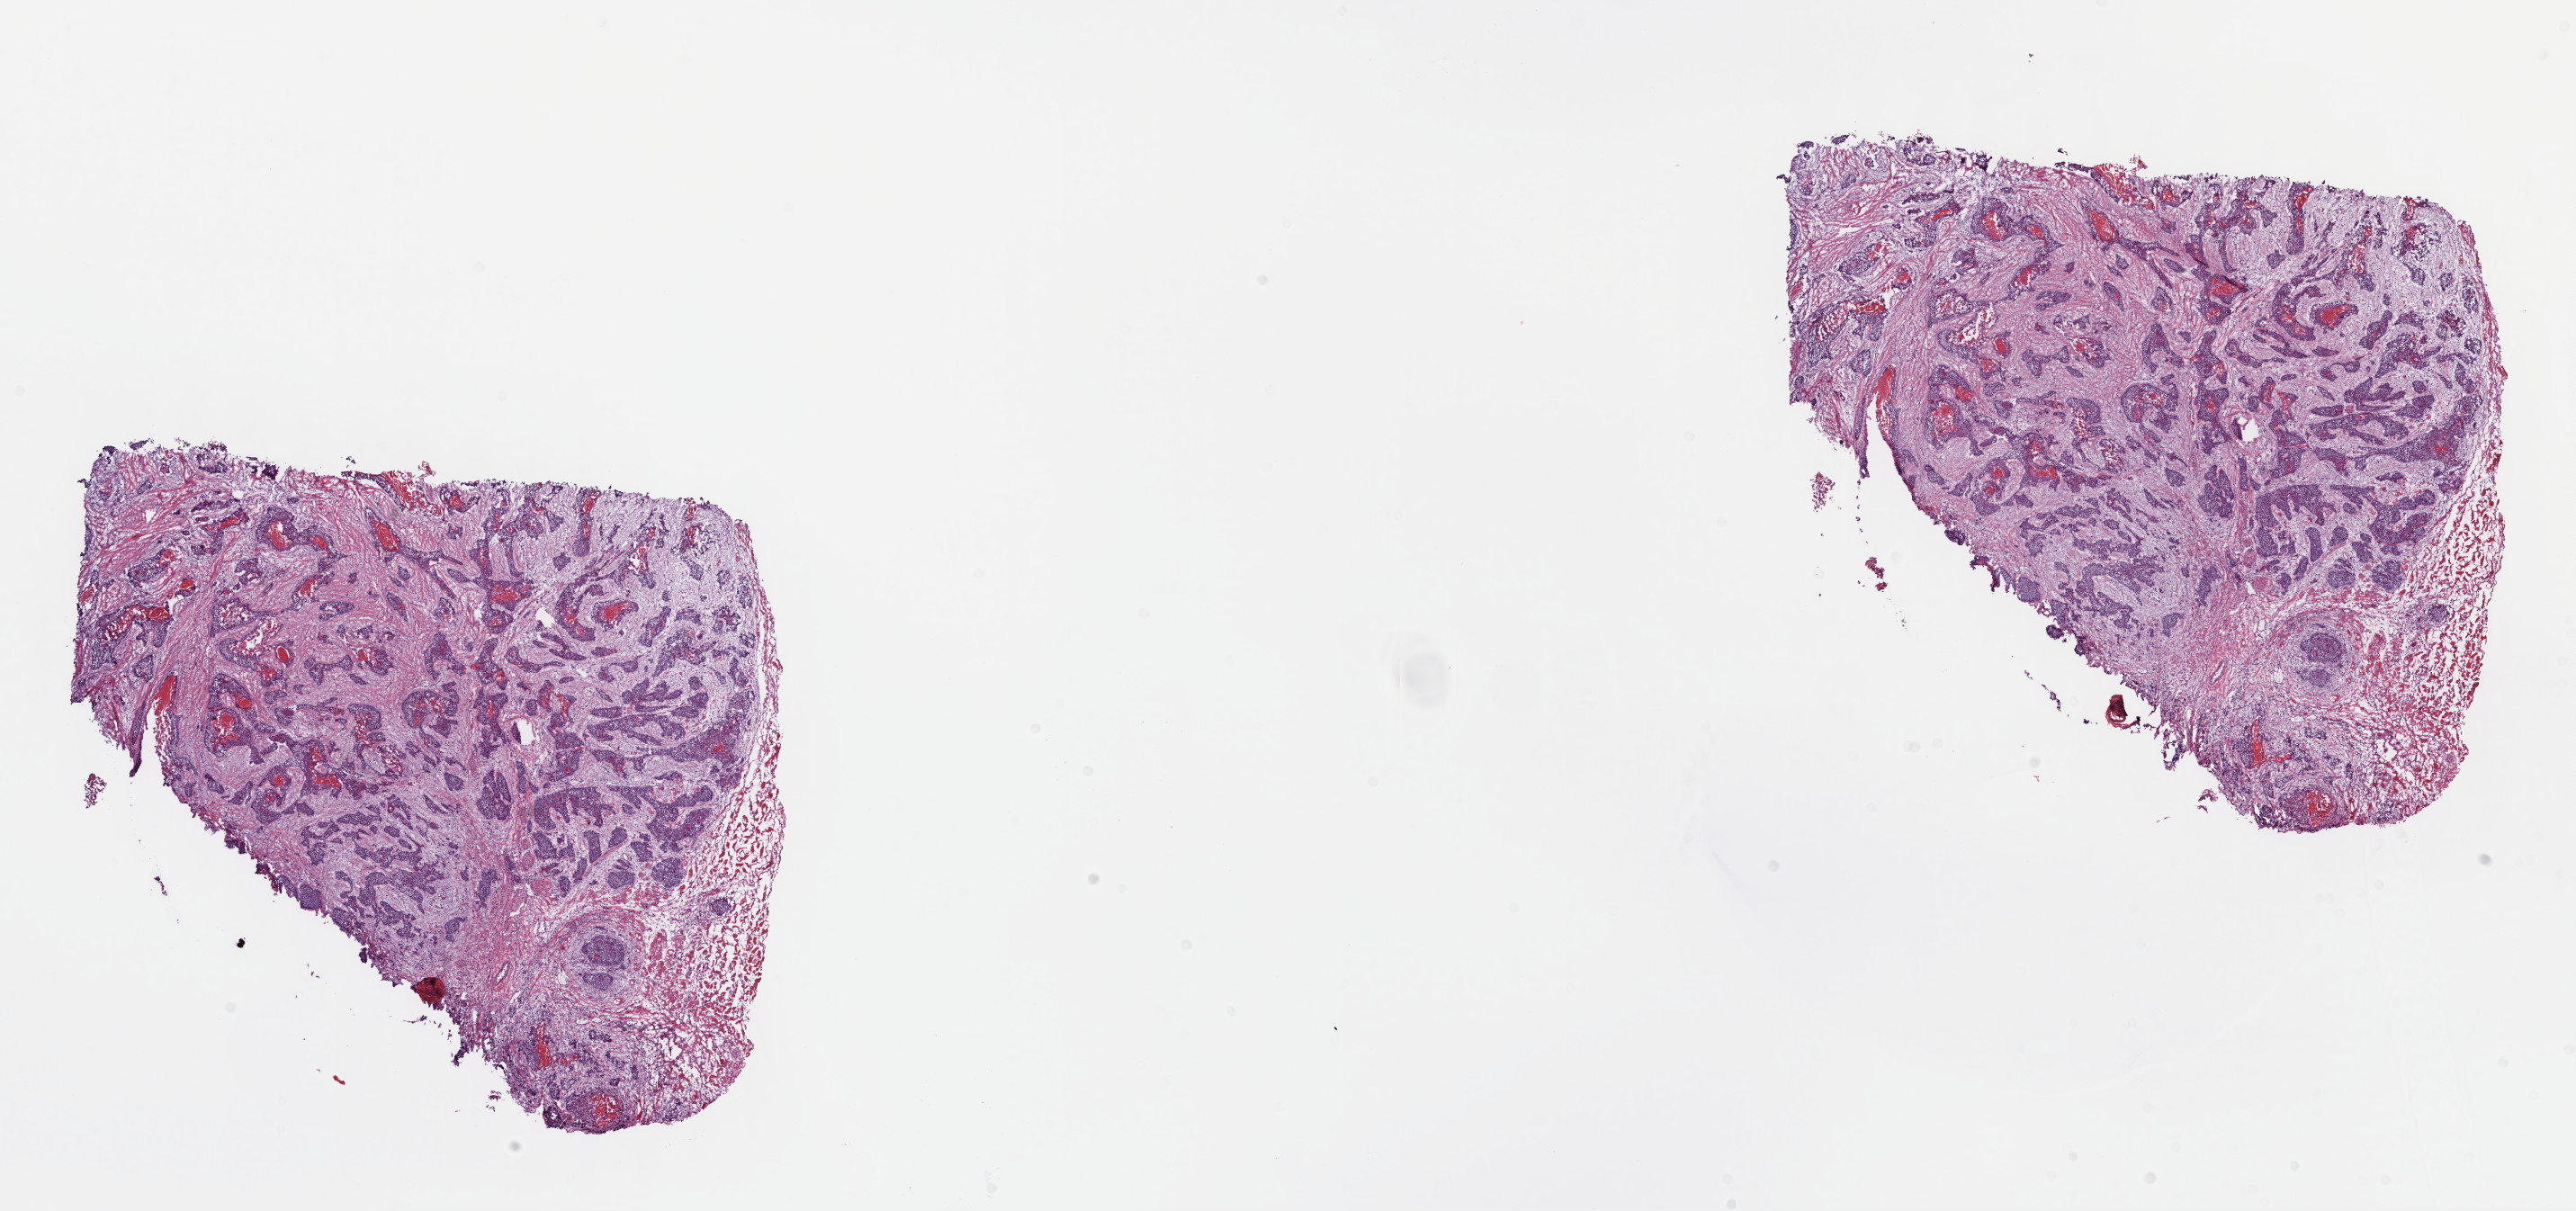
Digitized H&E-stained tissue section (whole slide) — whole scanned area (about 23.2 x 10.9 mm) shown as a low-resolution overview; frozen section from the top of the tissue portion; metastatic tumour sample, sampled site not recorded. Male patient; age at initial diagnosis 67 years. Composition of this section per pathologist review: tumour cells 60%, tumour nuclei 80%, normal cells 0%, stromal cells 40%, necrosis 0%. Infiltration values recorded for this section: lymphocyte infiltration 5%, monocyte infiltration 0%, neutrophil infiltration 0%.
* this section: metastatic tumour tissue
* patient diagnosis: Squamous cell carcinoma, NOS (primary site: floor of mouth, NOS)